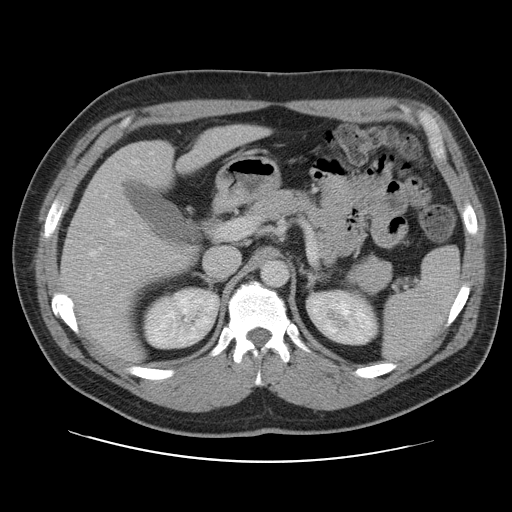
Contrast-enhanced abdominal CT, one axial slice. Slice 66 of 109 in the series (ordered by position). 120 kVp. Intravenous contrast given. Soft-tissue window (W 400 / L 40 HU). 5 mm slice thickness. 512 × 512 image matrix, field of view 402 × 402 mm. Male patient, age 35 years. Case-level facts recorded for this patient, not image findings: diagnosis: colorectal cancer liver metastases, imaged before liver resection; multiple liver metastases: yes; largest metastasis: 2.8 cm; chemotherapy before resection: yes.
Annotated regions visible in this slice (expert manual segmentation):
- hepatic veins: box from (x=91, y=252) to (x=110, y=312) px
- liver: (x=61, y=125)–(x=264, y=361)
- planned liver remnant (the part of the liver to remain after resection): (x=61, y=126)–(x=263, y=360)
- portal vein (with intrahepatic branches): (x=84, y=217)–(x=144, y=285)